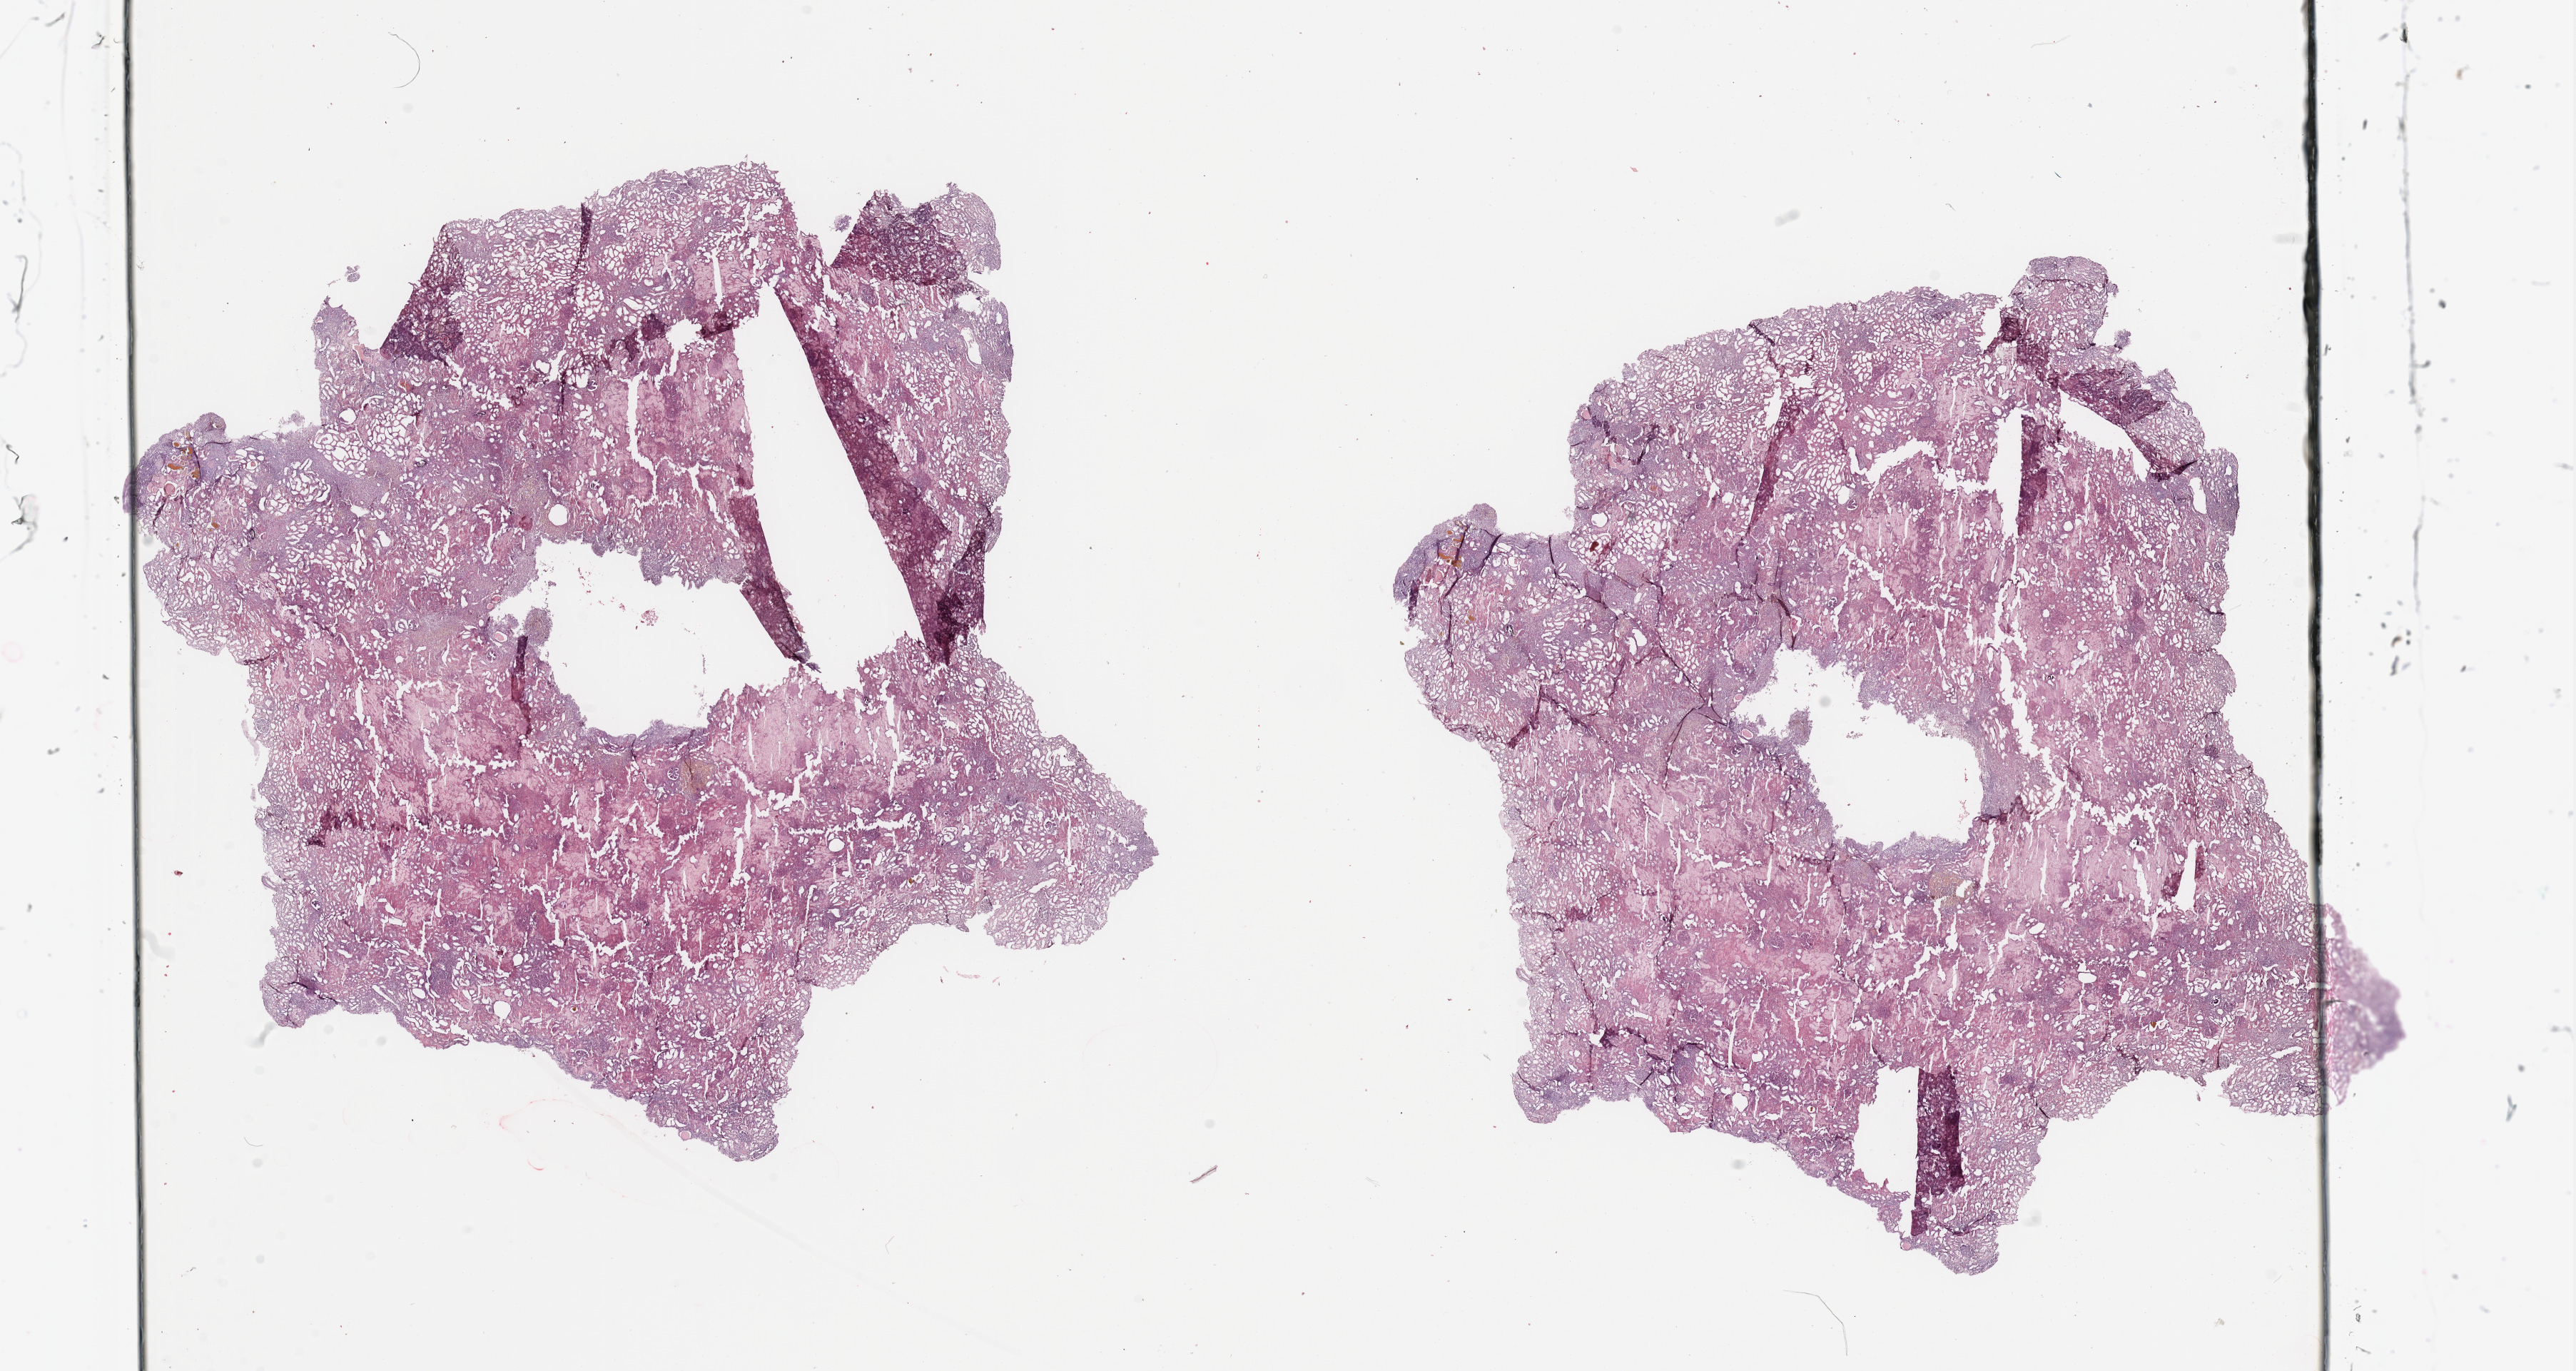
Hematoxylin and eosin (H&E) stained whole-slide image, whole scanned area (about 28.5 x 15.2 mm) shown as a low-resolution overview. Normal (non-tumour) tissue sample, sampled site: kidney. Female, 86 y/o.
This section: normal (non-tumour) tissue from the same patient. Patient diagnosis: Renal cell carcinoma, NOS.